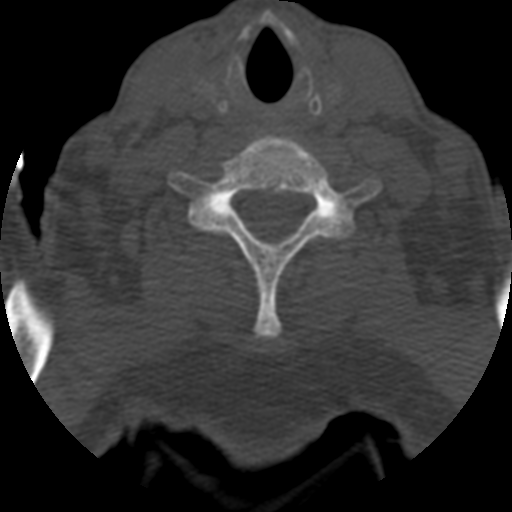
CT including the spine, one axial slice. Position 531 of 708 along the scan axis. One of 3 acquisitions stored at this slice position. Bone window (W 1800 / L 400 HU). 1.25 mm slice thickness. 512 × 512 image matrix. Patient age 55 years. From the clinical record (not read from this slice): primary cancer: colon; vertebrae with lytic lesions (as recorded): T12, L1, L5.
Outlined on this slice (semi-automatically segmented with operator editing):
- T1 vertebra: box from (x=216, y=198) to (x=240, y=222) px